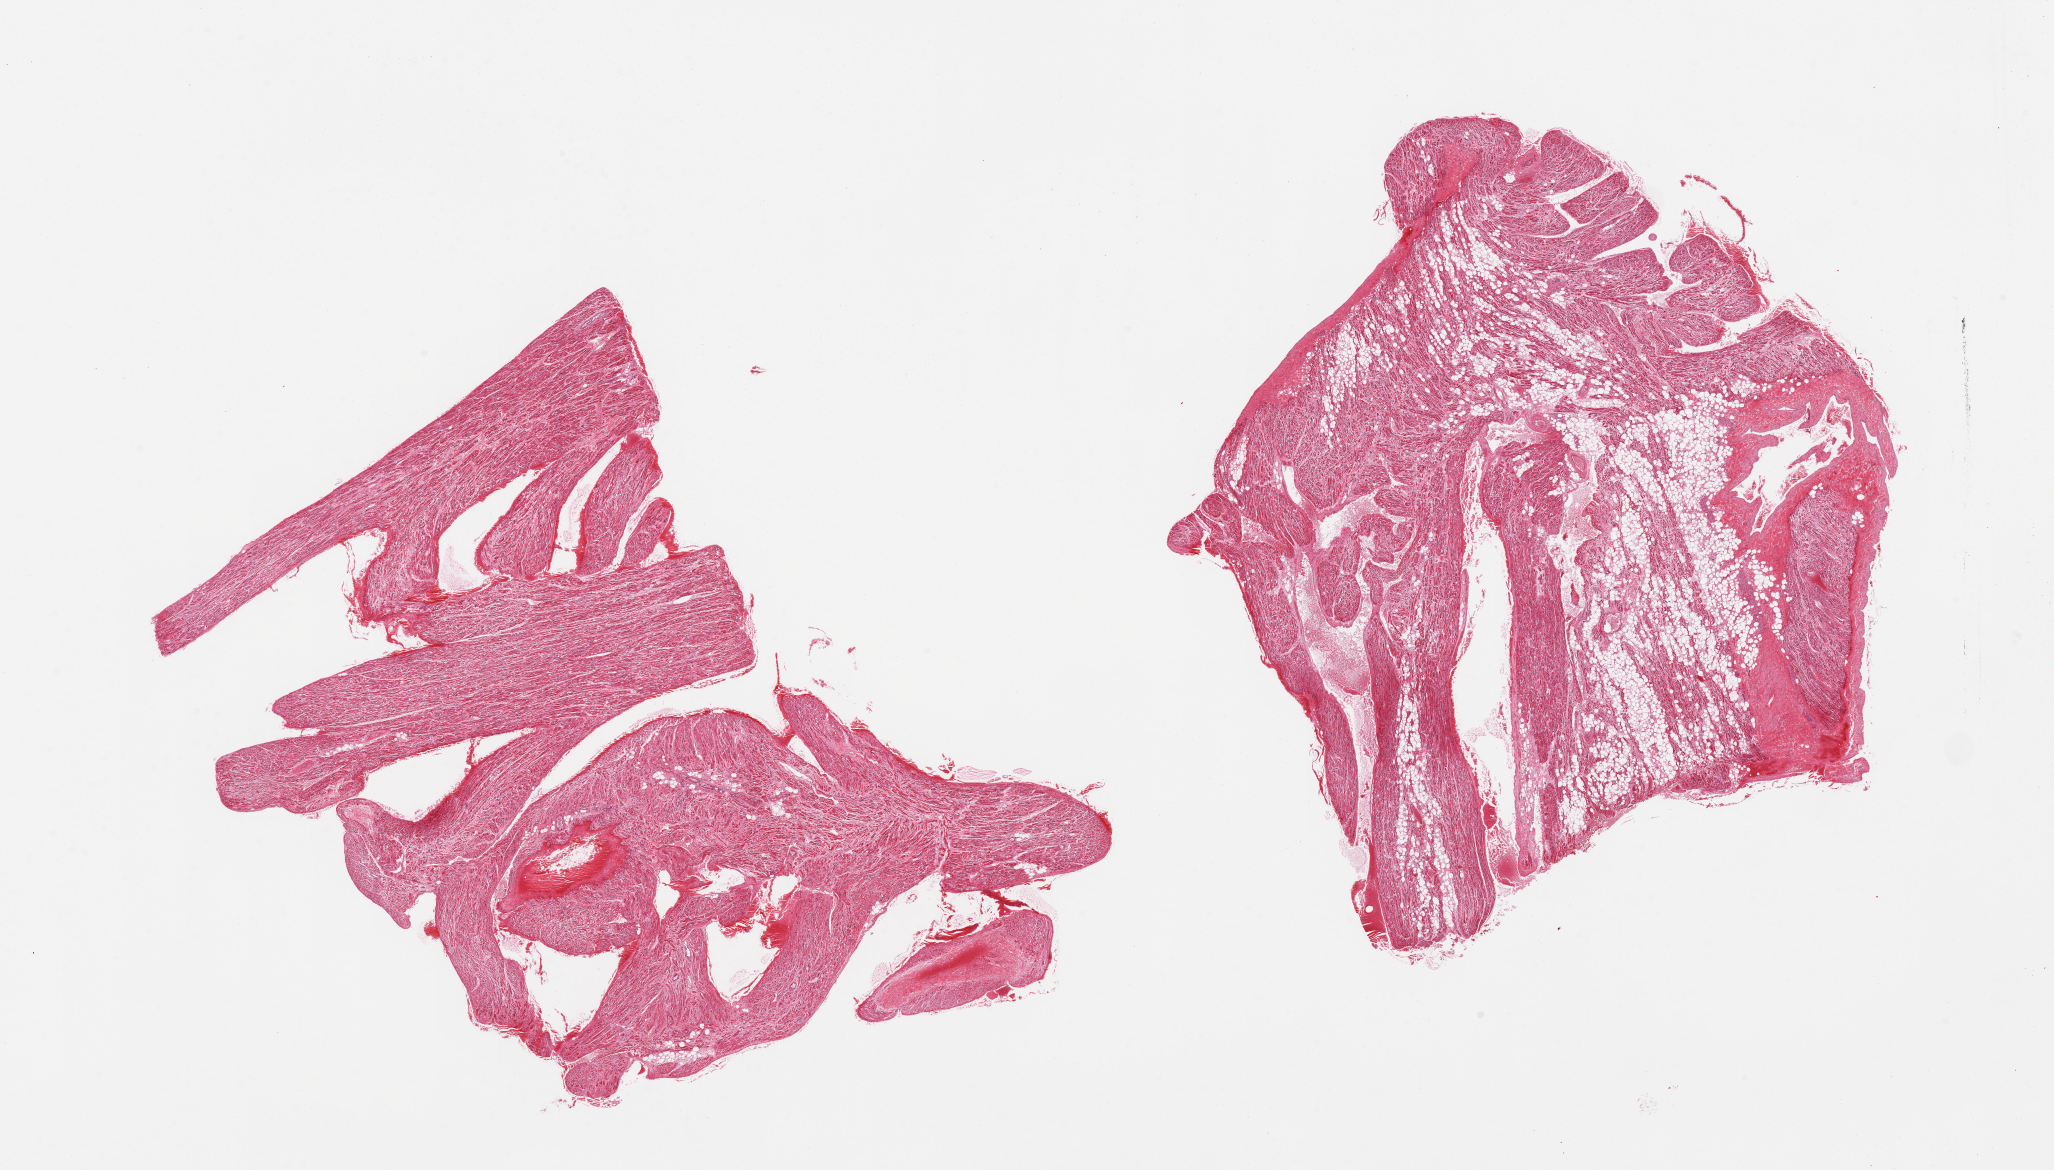
Hematoxylin and eosin (H&E) whole-slide image, a low-resolution overview of the entire scanned area, about 32.5 x 18.5 mm, PAXgene-fixed paraffin-embedded (PFPE) section, sampled site (target tissue): auricular appendage, donor tissue sample. Donor sex: male.
Pathologist's review note for this sample: 2 pieces, no abnormalities.